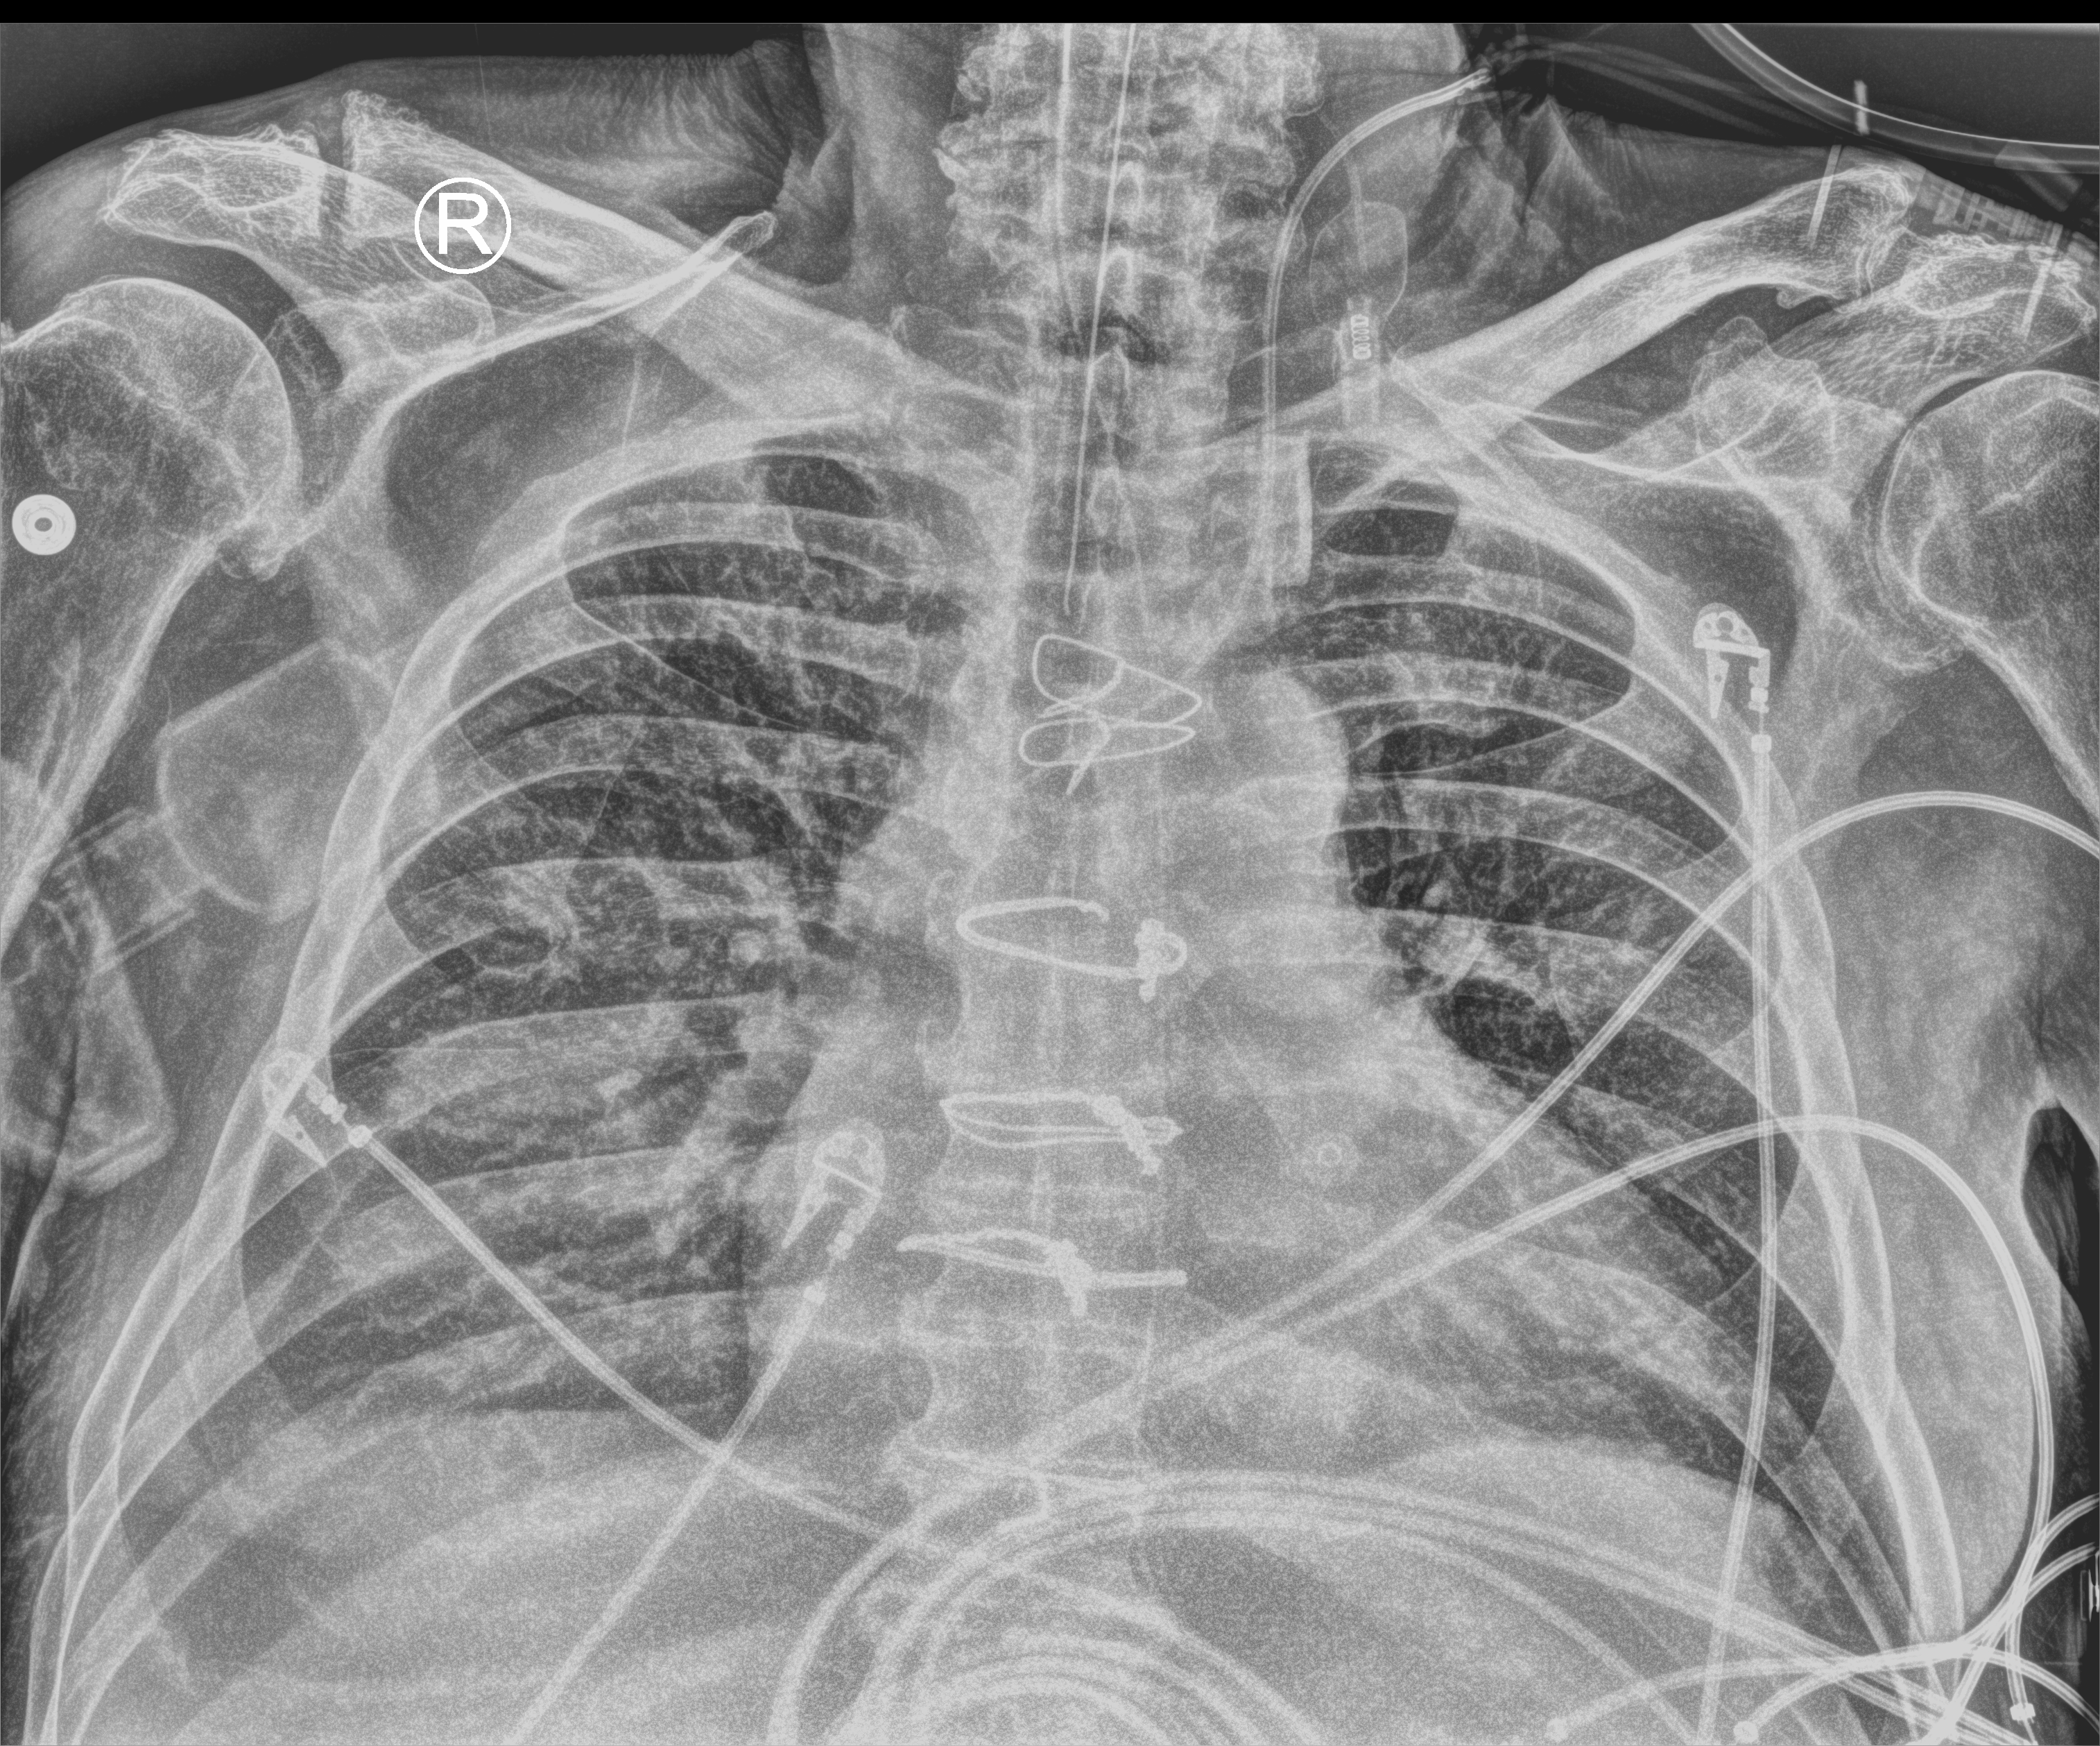
Chest X-ray (portable); anteroposterior (AP) projection. Patient hospitalised with COVID-19; male, aged 60–74 years.
Admission-level facts for this patient (not findings on this image; timing relative to this image not recorded):
- hypertension (admission record): yes
- admitted to intensive care during this hospital stay: yes